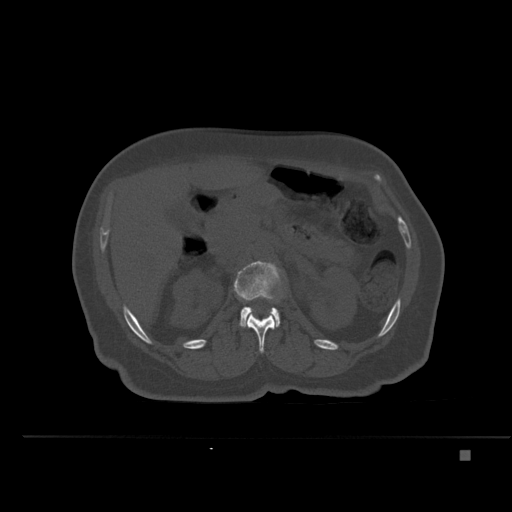
CT including the spine, one axial slice. Slice 228 of 477 in the series (ordered by position). Bone window (W 1800 / L 400 HU). 512 × 512 image matrix, field of view 422 × 422 mm. Patient: female, 74 years. Case-level facts recorded for this patient, not image findings: primary cancer: colon.
Structures marked on this image (semi-automatically segmented with operator editing):
- L1 vertebra: box from (x=246, y=313) to (x=276, y=353) px
- L2 vertebra: (x=234, y=261)–(x=280, y=327)